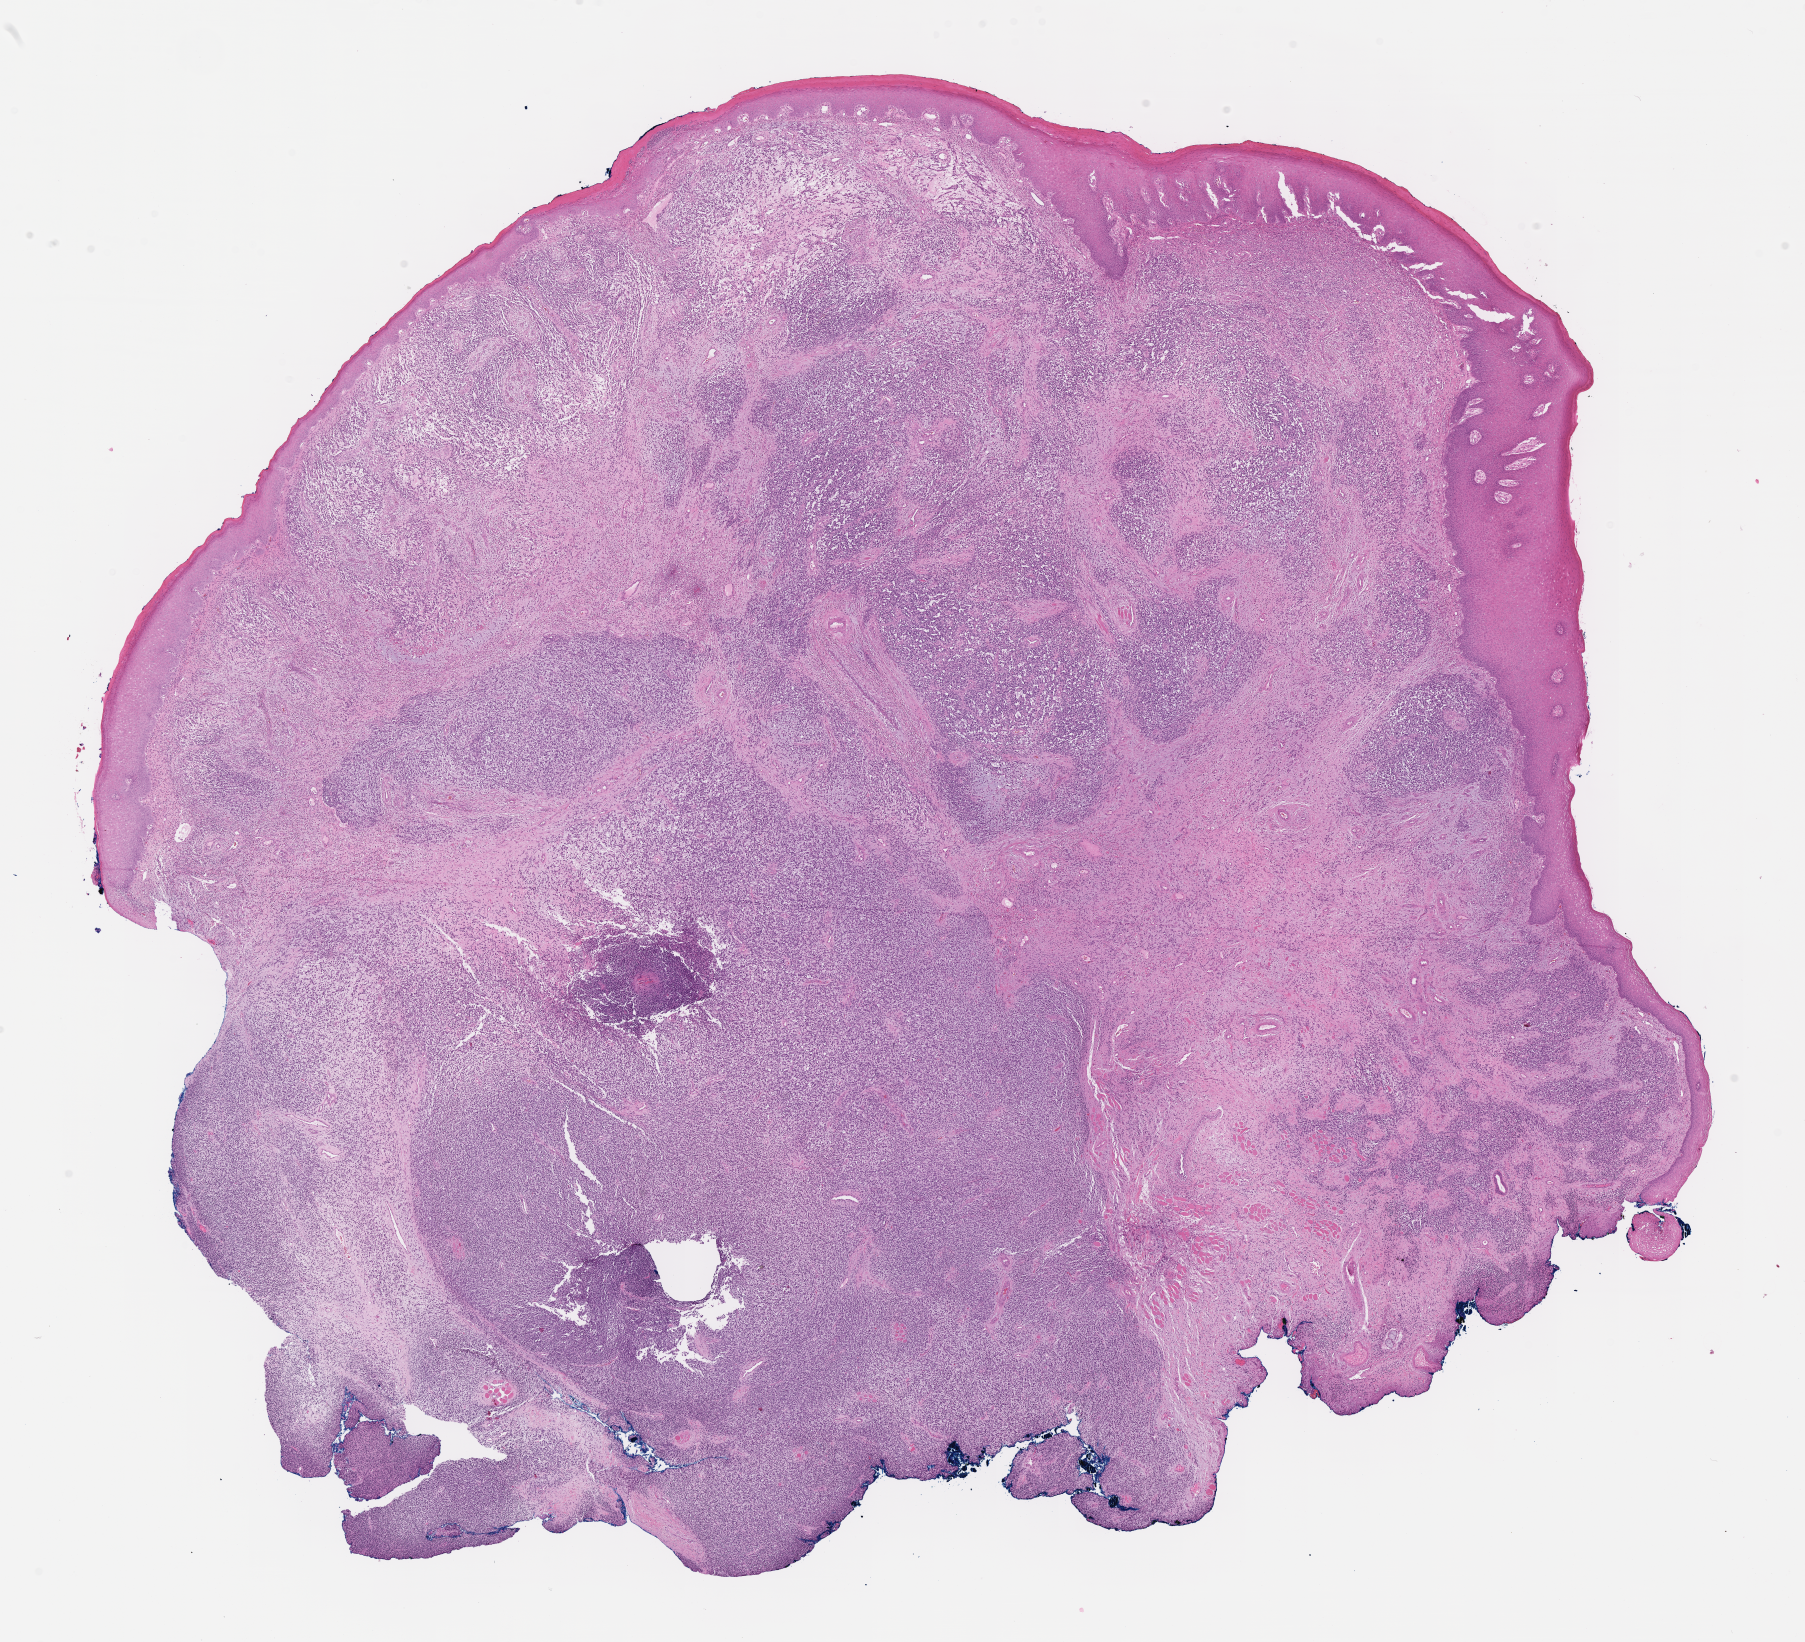
Hematoxylin and eosin (H&E) whole-slide image of tumor tissue — shown as a low-resolution overview of the whole scanned area (about 14.6 x 13.3 mm). Formalin-fixed, paraffin-embedded (FFPE) tissue. Sample anatomic site: soft palate, left. Patient: male, age 10.1 years at diagnosis.
Diagnosis: rhabdomyosarcoma; histological classification: embryonal rhabdomyosarcoma.